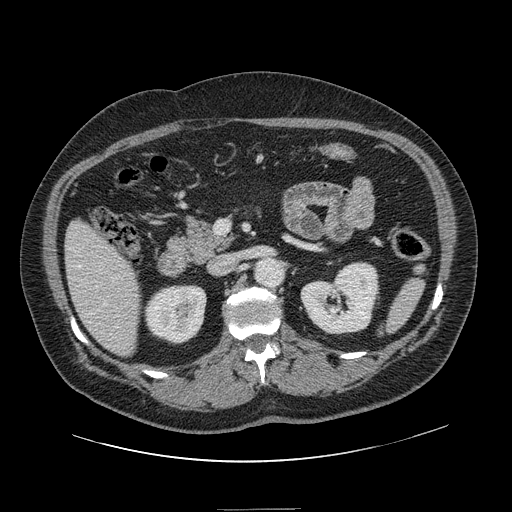
Contrast-enhanced abdominal CT, one axial slice. 120 kVp. Intravenous contrast given. Soft-tissue window (W 400 / L 40 HU). 512 × 512 image matrix. Male patient, age 61 years. From the clinical record (not read from this slice): diagnosis: colorectal cancer liver metastases, imaged before liver resection; multiple liver metastases: yes.
Outlined on this slice (manually delineated by an expert):
- hepatic veins: box from (x=78, y=265) to (x=107, y=306) px
- liver: (x=66, y=222)–(x=141, y=355)
- planned liver remnant (the part of the liver to remain after resection): (x=66, y=222)–(x=141, y=356)